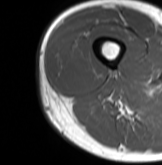
MRI of an extremity soft-tissue mass, one axial slice. Position 19 of 61 along the scan axis. MR volume resampled by the dataset authors to the PET/CT grid (not the native acquisition matrix). 162 × 165 image matrix. Male patient. Case-level facts recorded for this patient, not image findings: histological type: poorly differentiated synovial sarcoma; grade: high; site of the primary tumour: right buttock.
Structures marked on this image (expert contour drawn on MRI and transferred to this co-registered scan by the dataset authors):
- gross tumour volume including surrounding oedema: bounding box <55,45,101,89> (left, top, right, bottom; pixels)